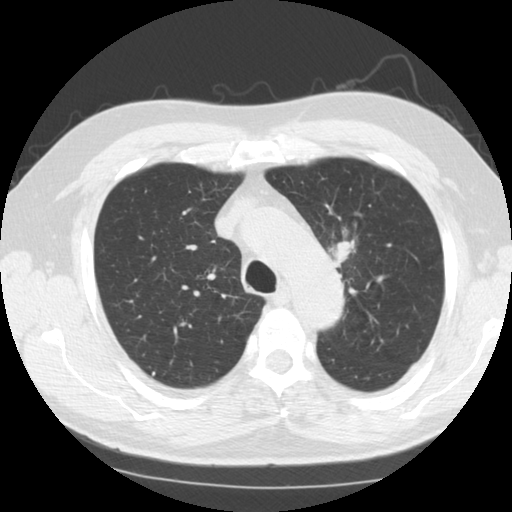
Low-dose screening chest CT, axial slice, third annual screen, lung window (W 1500 / L -600 HU), 2.5 mm slice thickness, 120 kVp, slice 30 of 124 in the series. Male, age 60 years at enrolment.
Expert reader's lesion annotation, bounding box <319,229,371,291> (left, top, right, bottom; pixels). Screening reader's record for this exam (one nodule recorded; not confirmed to be the boxed lesion): non-calcified nodule or mass ≥4 mm, left upper lobe, 24 × 21 mm, smooth margins, soft tissue attenuation, pre-existing on the prior screen: no. Participant outcome: lung cancer diagnosed 14 days after this screen — small cell carcinoma, NOS, left upper lobe, stage IIA (AJCC 6th edition), 26 mm at pathology.